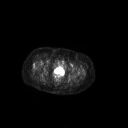
FDG PET of an extremity soft-tissue mass (from a PET/CT study), one axial slice; slice 64 of 267 in the series (ordered by position); 3.27 mm slice thickness; 128 × 128 image matrix, field of view 700 × 700 mm. Female patient, age 70 years. From the clinical record (not read from this slice): histological type: synovial sarcoma; grade: intermediate; site of the primary tumour: right buttock.
Structures marked on this image (expert contour drawn on MRI and transferred to this co-registered scan by the dataset authors):
- gross tumour volume including surrounding oedema: bounding box (x1, y1, x2, y2) in pixels: (38, 76, 41, 78)